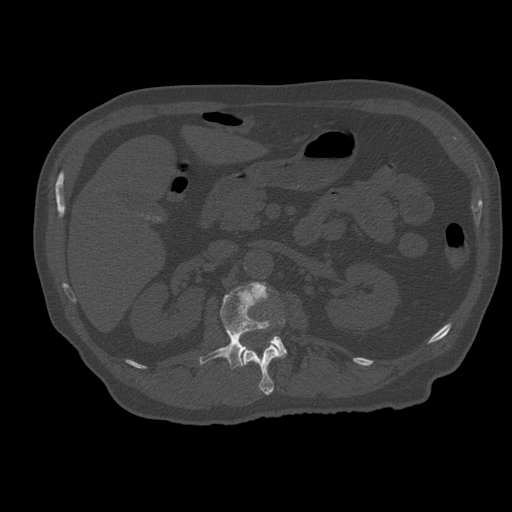
CT including the spine, one axial slice; slice 225 of 399 in the series (ordered by position); reconstruction kernel STANDARD; 120 kVp; bone window (W 1800 / L 400 HU); 1.25 mm slice thickness; 512 × 512 image matrix, field of view 407 × 407 mm. Patient age 73 years. Case-level facts recorded for this patient, not image findings: primary cancer: prostate; vertebrae with lytic lesions (as recorded): L2.
Annotated regions visible in this slice (semi-automatic segmentation, software-assisted and operator-edited):
- L1 vertebra: bounding box [x1, y1, x2, y2] px = [241, 340, 280, 395]
- L2 vertebra: [200, 282, 287, 369]